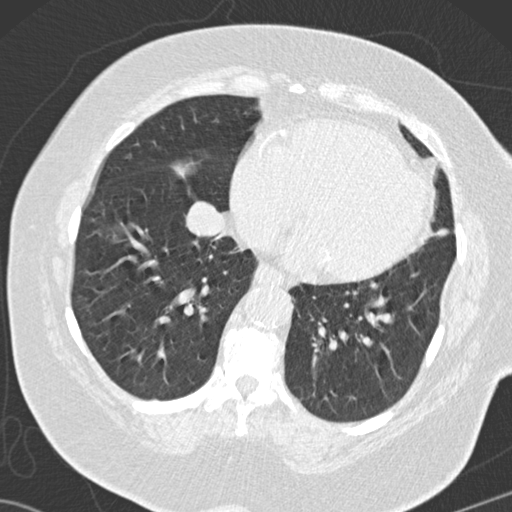
Low-dose screening chest CT, one axial slice. Position 49 of 146 along the scan axis. Reconstruction kernel B30f. Lung window (W 1500 / L -600 HU). 512 × 512 image matrix, field of view 350 × 350 mm.
Outlined on this slice (manually delineated by an expert):
- lesion 3 (tumor, lower lobe of right lung): bounding box [x1, y1, x2, y2] px = [185, 202, 225, 237]